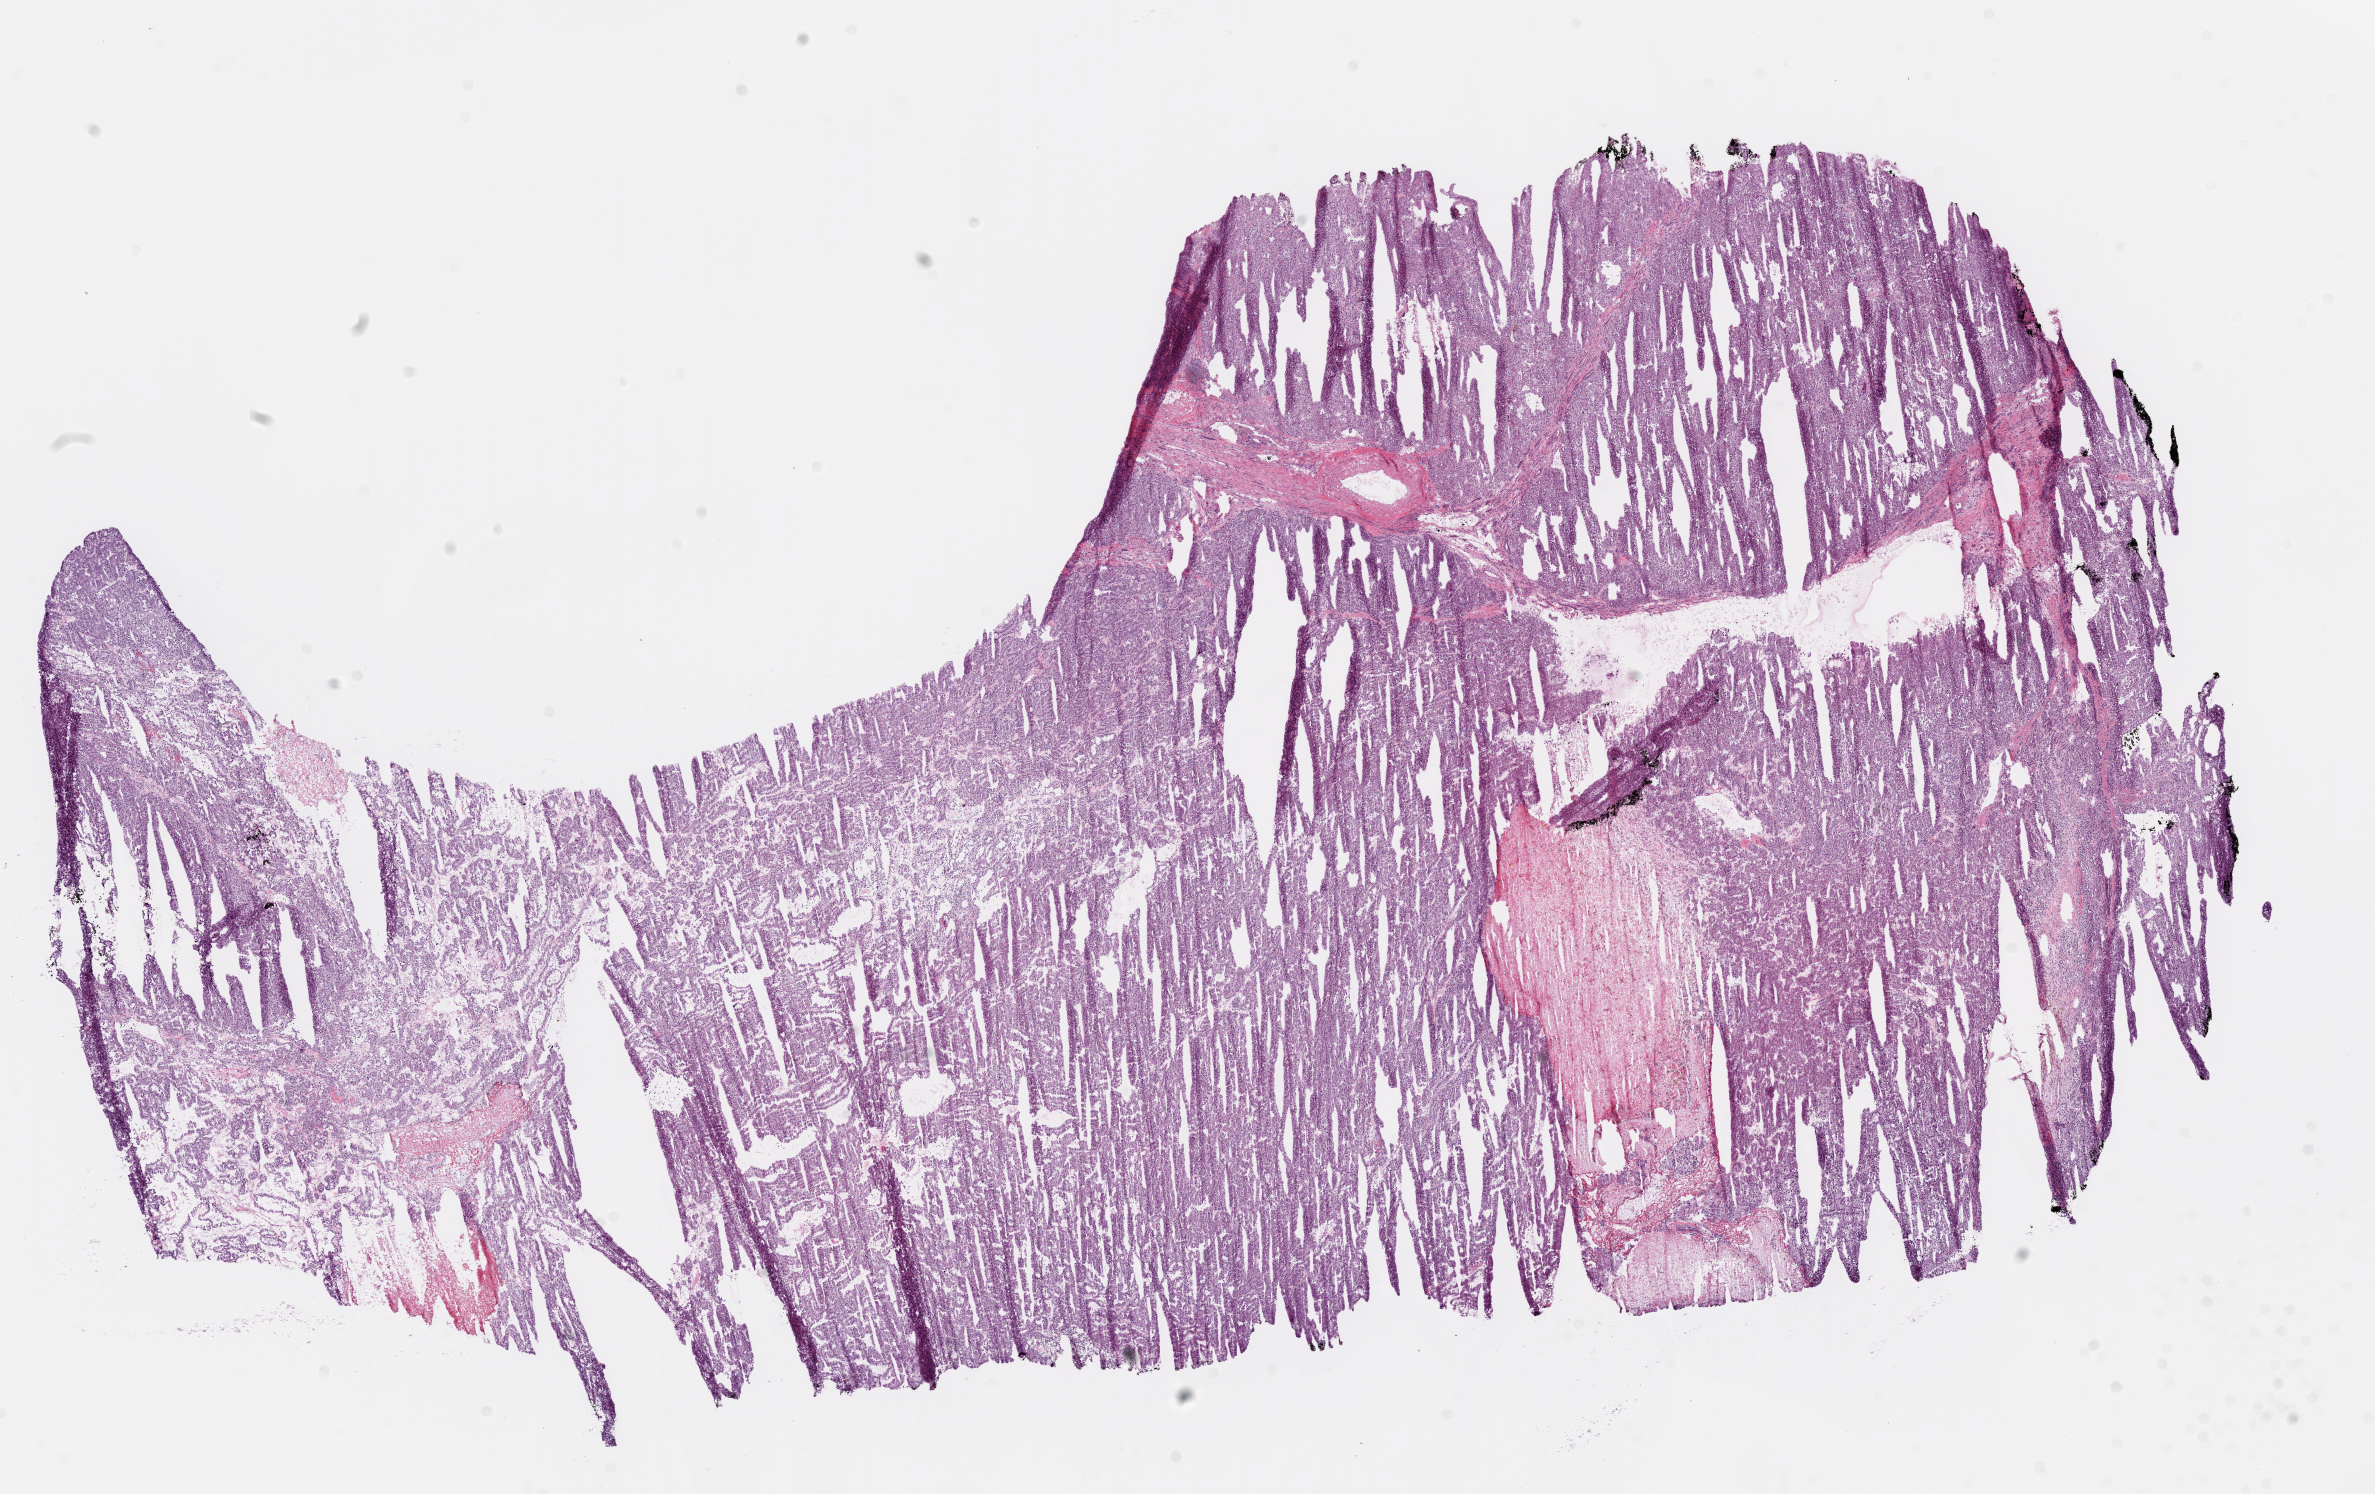
Digitized H&E-stained tissue section (whole slide), whole scanned area (about 19.1 x 12.0 mm, acquisition: 20x scan) shown as a low-resolution overview; frozen section; primary tumour sample from the kidney. Patient: male, age at initial diagnosis 59 years. Slide review estimates, as recorded: tumour cells 80%, tumour nuclei 85%.
Diagnosis: Clear cell adenocarcinoma, NOS.